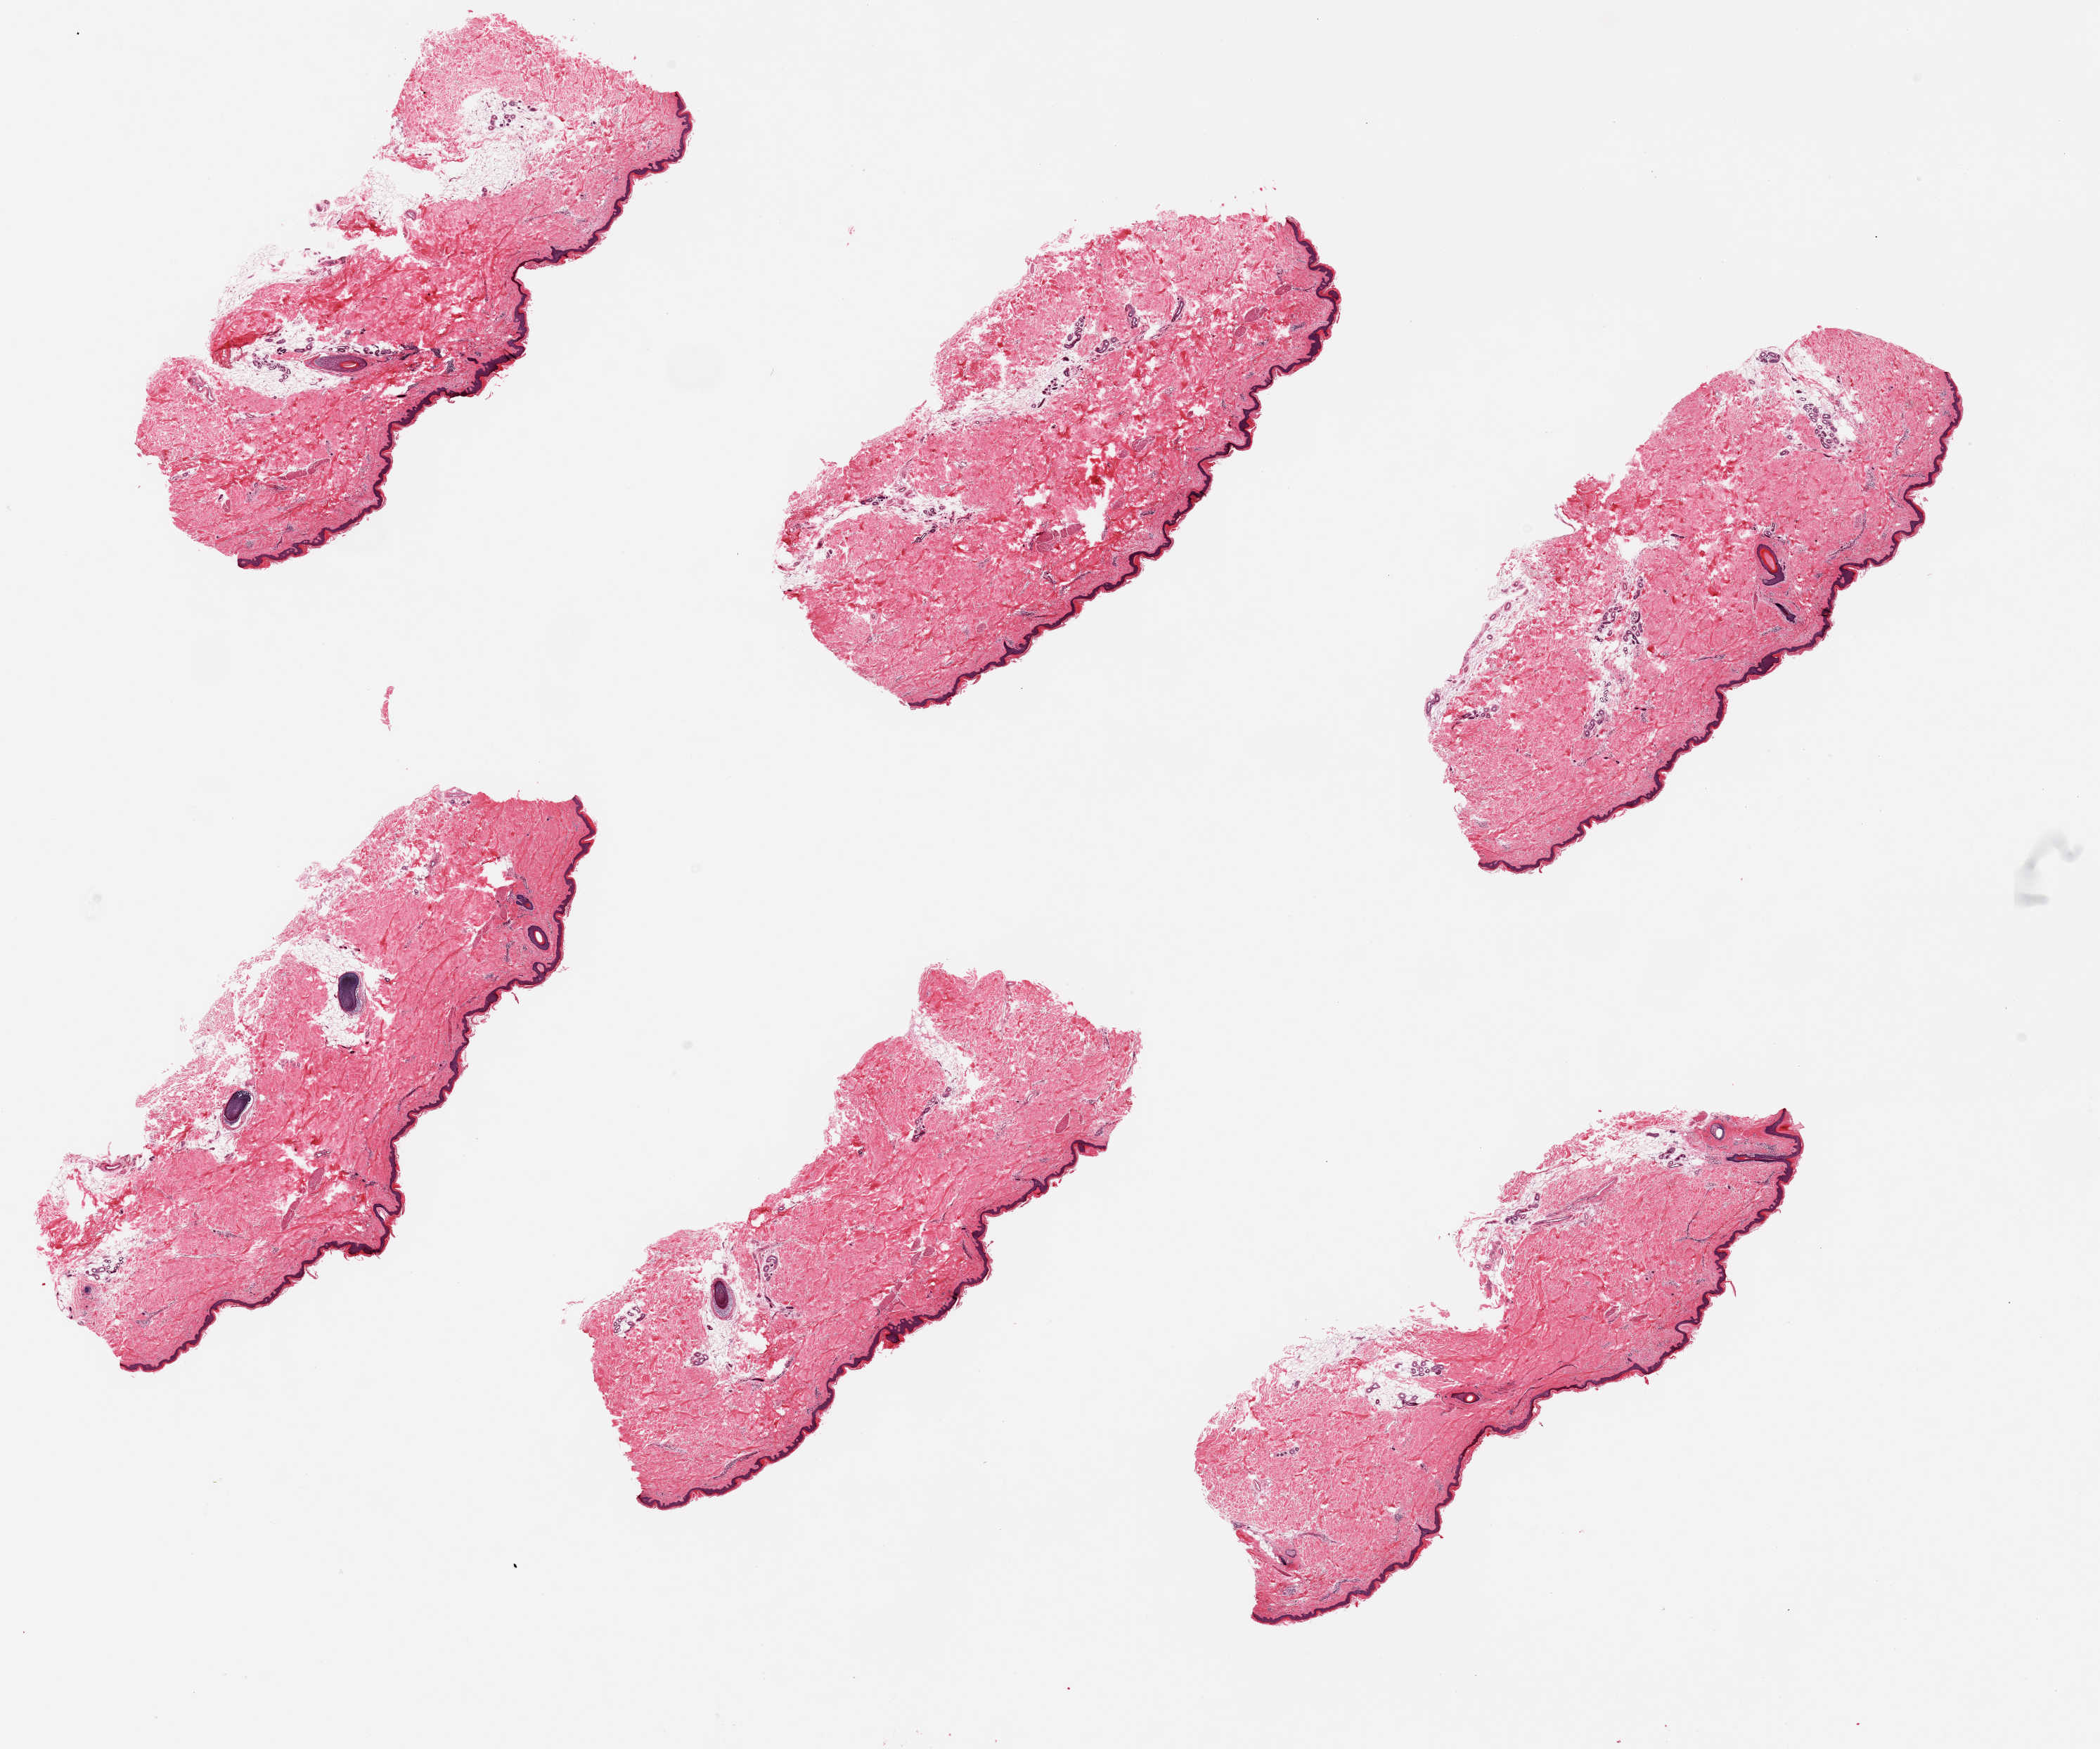
Whole-slide image, hematoxylin and eosin (H&E) stain — low-resolution overview of the scanned area, about 23.6 x 19.7 mm (from a 20x scan); PAXgene-fixed paraffin-embedded (PFPE) section; target tissue: skin of lower leg; donor tissue sample. Donor sex: male.
• review note (as recorded): 6 pieces, dermal fat present in several sections, squamous epithelium is ~40-50 microns thick